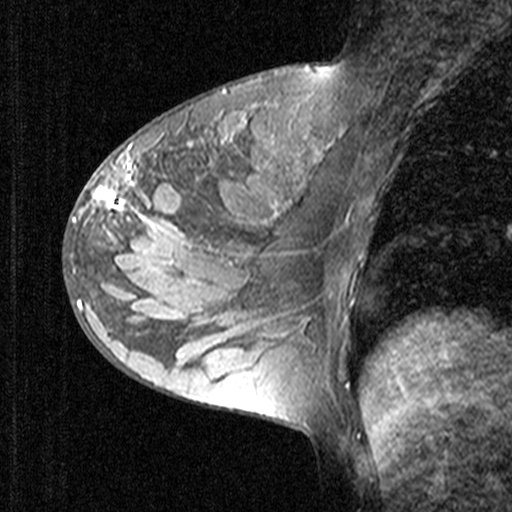
Breast MRI (dynamic contrast-enhanced), one sagittal slice; position 20 of 44 along the scan axis; dynamic contrast-enhanced study with each time point stored as its own series, time point 2 of 3 at this slice position (early post-contrast, ordered by acquisition time); 1.5 T; TE 4.5 ms, TR 11 ms; 3 mm slice thickness; 512 × 512 image matrix. Patient: female, 27 years. From the clinical record (not read from this slice): setting: breast cancer imaged before/during neoadjuvant chemotherapy; receptor status: HR-positive, HER2-negative.
Outlined on this slice (semi-automatic segmentation, software-assisted and operator-edited):
- analysis volume of interest (the breast-tissue region the enhancement analysis was run in; not a lesion): bounding box (x1, y1, x2, y2) in pixels: (68, 146, 165, 239)
- tumour enhancement mask (voxels above the 90 % enhancement threshold inside the analysis volume of interest): (72, 146, 137, 223)